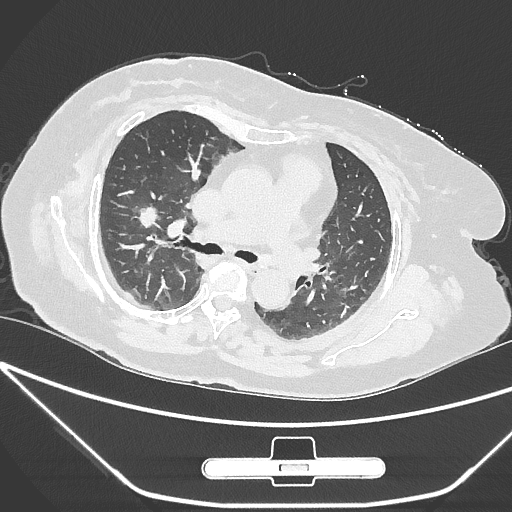
Chest CT, one axial slice. Position 164 of 245 along the scan axis. 120 kVp. Lung window (W 1500 / L -600 HU). 1 mm slice thickness. 512 × 512 image matrix. Patient: female, 65 years. From the clinical record (not read from this slice): clinical TNM (as recorded): T1c N0 M0; histopathological grade: G3.
Annotated regions visible in this slice (rectangle marked by the reading radiologist):
- lung tumour (recorded histology: adenocarcinoma): bounding box [x1, y1, x2, y2] px = [134, 196, 159, 235]